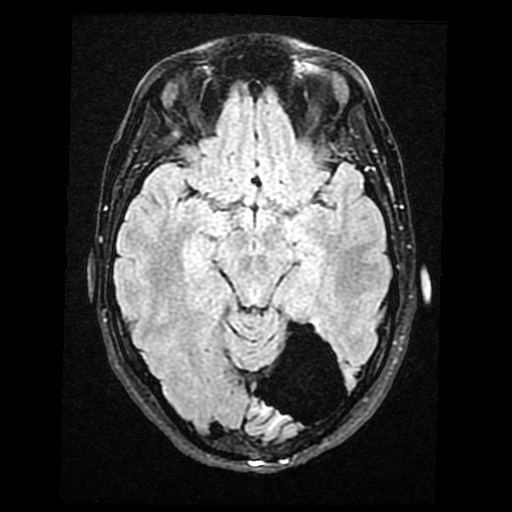
Brain MRI from a brain-tumour surgery series, one axial slice; slice 25 of 40 in the series (ordered by position); T2 FLAIR; 512 × 512 image matrix, field of view 240 × 240 mm. From the clinical record (not read from this slice): histopathology: Glioma with ependymal features; WHO grade: 2; tumour location: Left Parietal.
Structures marked on this image (outlined manually by an expert reader):
- tumour: box from (x=310, y=312) to (x=321, y=330) px